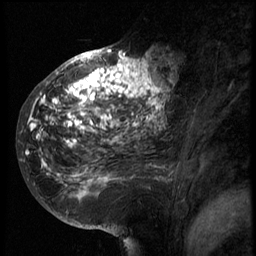
Breast MRI (dynamic contrast-enhanced), one sagittal slice. Slice 34 of 66 in the series (ordered by position). 3 images stored at this slice position (order not interpretable as contrast timing). 1.5 T. TE 4.2 ms, TR 8.9 ms. 2.5 mm slice thickness. 256 × 256 image matrix. Female patient, age 39 years. Case-level facts recorded for this patient, not image findings: setting: breast cancer imaged before/during neoadjuvant chemotherapy; receptor status: HER2-positive.
Outlined on this slice (semi-automatically segmented with operator editing):
- analysis volume of interest (the breast-tissue region the enhancement analysis was run in; not a lesion): bounding box <29,44,166,196> (left, top, right, bottom; pixels)
- tumour enhancement mask (voxels above the 140 % enhancement threshold inside the analysis volume of interest): <29,49,166,182>